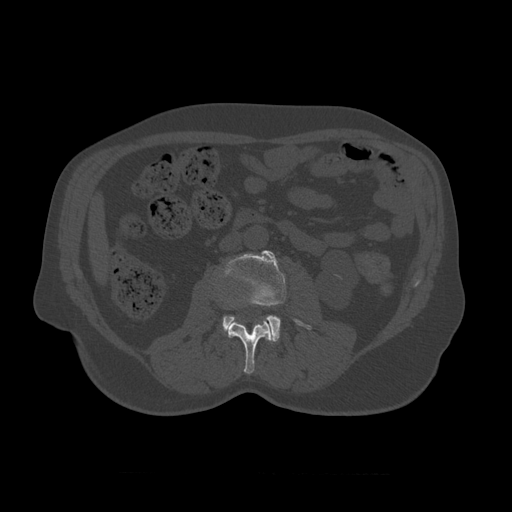
CT including the spine, one axial slice. Position 318 of 450 along the scan axis. Bone window (W 1800 / L 400 HU). 512 × 512 image matrix. Patient age 75 years. From the clinical record (not read from this slice): primary cancer: prostate.
Outlined on this slice (semi-automatically segmented with operator editing):
- L2 vertebra: bounding box (x1, y1, x2, y2) in pixels: (228, 317, 273, 375)
- L3 vertebra: (223, 250, 312, 343)